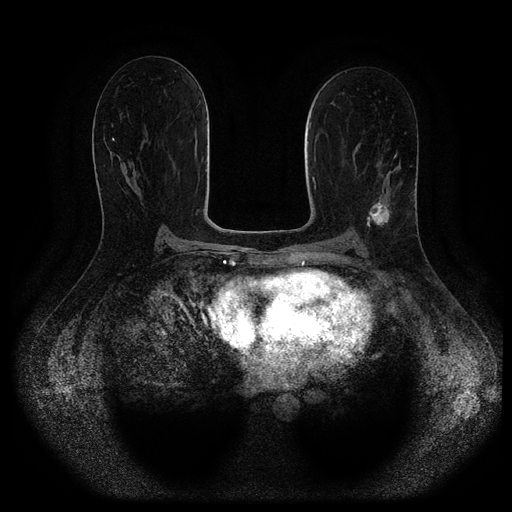
Breast MRI (dynamic contrast-enhanced, multi-phase), one axial slice; position 57 of 116 along the scan axis; dynamic contrast-enhanced series, time point 2 of 5 at this slice position (early post-contrast); 1.5 T; TE 2.6 ms, TR 5.3 ms; 2 mm slice thickness; 512 × 512 image matrix. Patient: female, 45 years.
Outlined on this slice (semi-automatic segmentation, software-assisted and operator-edited):
- breast lesion (labelled 'tumour' in the annotation; benign lesions carry a separate 'benign' label): box from (x=368, y=198) to (x=392, y=227) px